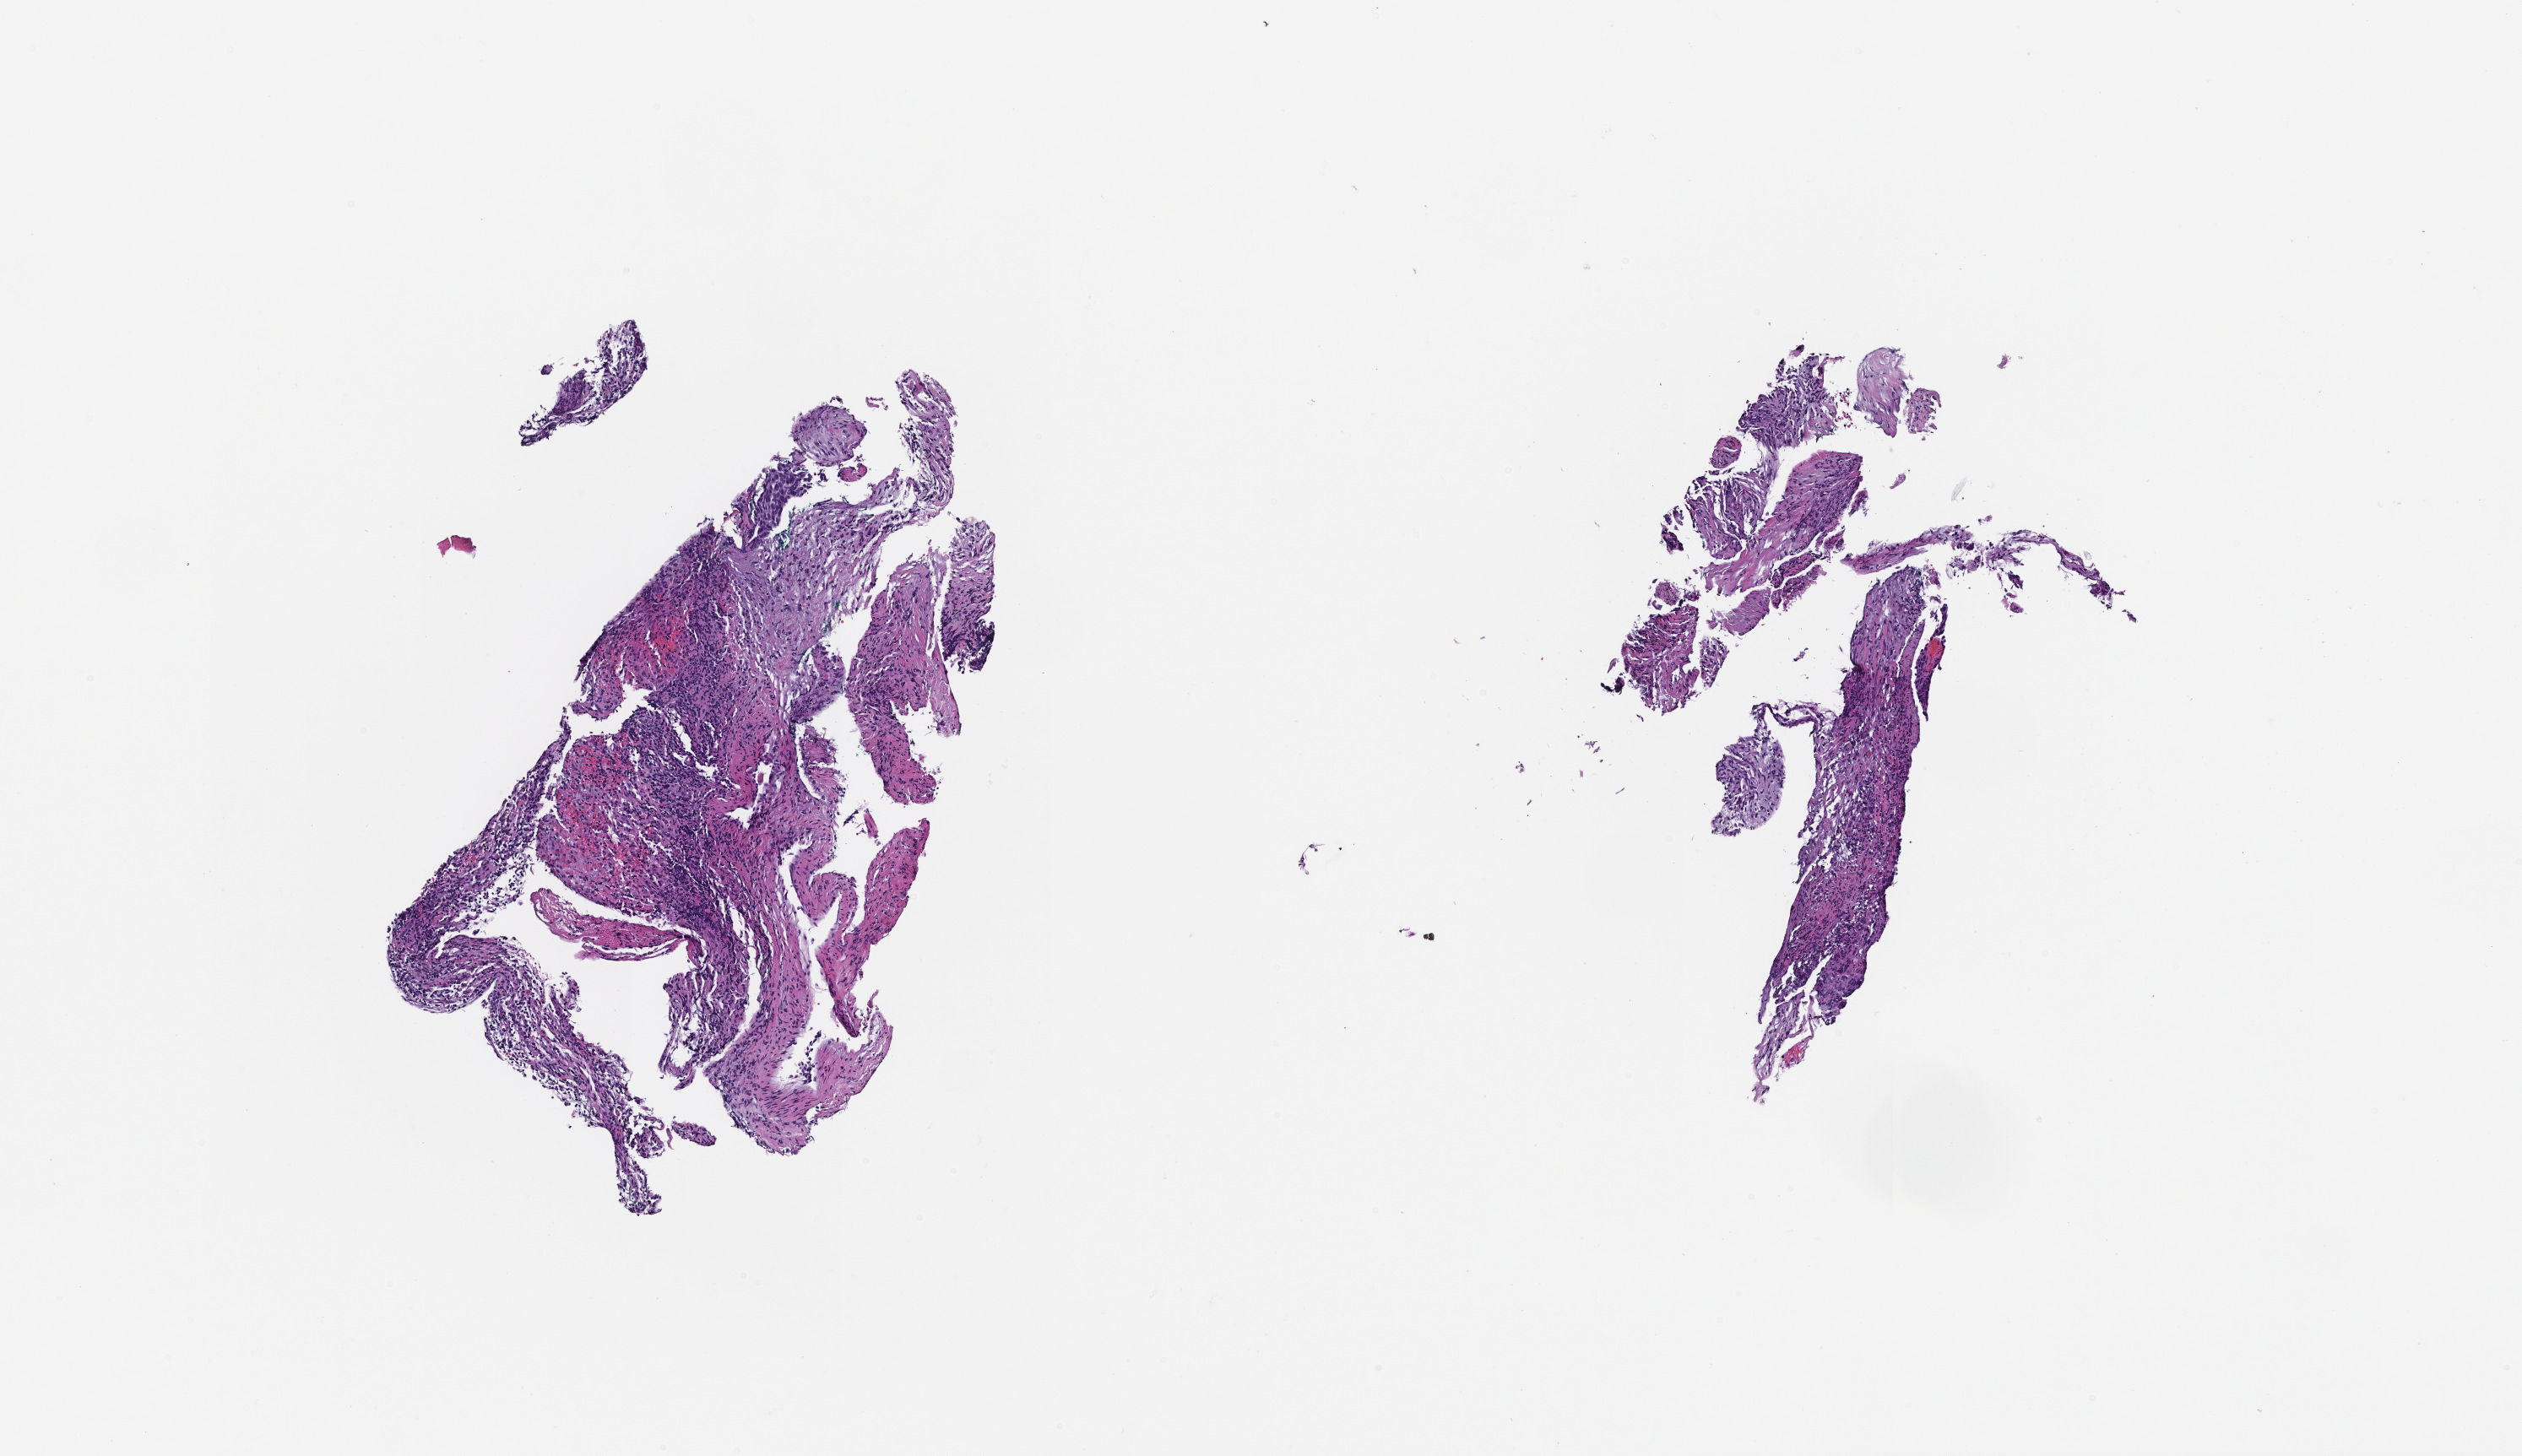
Whole-slide image, hematoxylin and eosin (H&E) stain — whole scanned area (about 6.0 x 3.5 mm) shown as a low-resolution overview. FFPE section. Female patient.
• this section: metastatic tumor tissue
• primary diagnosis of the patient: Non-Small Cell Lung Carcinoma